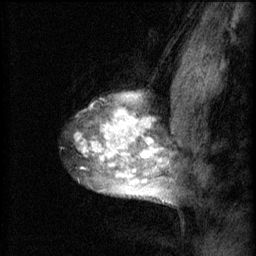
Breast MRI (dynamic contrast-enhanced), one sagittal slice; slice 47 of 60 in the series (ordered by position); 3 images stored at this slice position (order not interpretable as contrast timing); 1.5 T; TE 4.2 ms, TR 8.2 ms; 2 mm slice thickness; 256 × 256 image matrix, field of view 180 × 180 mm. Female patient, age 40 years.
Annotated regions visible in this slice (semi-automatically segmented with operator editing):
- analysis volume of interest (the breast-tissue region the enhancement analysis was run in; not a lesion): bounding box (x1, y1, x2, y2) in pixels: (70, 84, 167, 205)
- tumour enhancement mask (voxels above the 70 % enhancement threshold inside the analysis volume of interest): (75, 92, 167, 203)